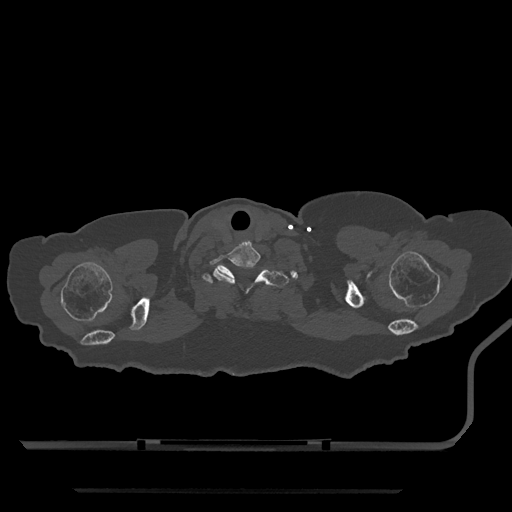
CT including the spine, one axial slice; position 725 of 797 along the scan axis; 120 kVp; bone window (W 1800 / L 400 HU); 0.5 mm slice thickness; 512 × 512 image matrix, field of view 440 × 440 mm. Patient: female, 51 years. Case-level facts recorded for this patient, not image findings: primary cancer: neuro.
Annotated regions visible in this slice (semi-automatically segmented with operator editing):
- T1 vertebra: bounding box [x1, y1, x2, y2] px = [202, 265, 289, 294]